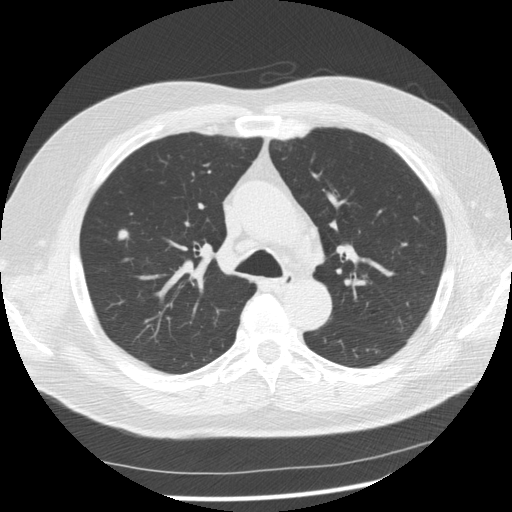
Low-dose screening chest CT, axial slice; second screening round (one year after baseline); lung window (W 1500 / L -600 HU); 2.5 mm slice thickness. Male participant, aged 61 years at enrolment. Current smoker at enrolment.
Lesion marked by an expert reader, box from (x=102, y=222) to (x=137, y=252) px. Screening reader's record for this exam (one nodule recorded; not confirmed to be the boxed lesion): non-calcified nodule or mass ≥4 mm, right upper lobe, 7 × 7 mm, smooth margins, soft tissue attenuation, pre-existing on the prior screen: yes; interval growth: no. Official screen result: positive, no significant change: stable abnormalities potentially related to lung cancer, unchanged since the prior screening exam. Later outcome: lung cancer diagnosed 389 days after this screen (after the third annual screen) — adenocarcinoma, NOS, right upper lobe, stage IIIA (AJCC 6th edition), 13 mm at pathology.